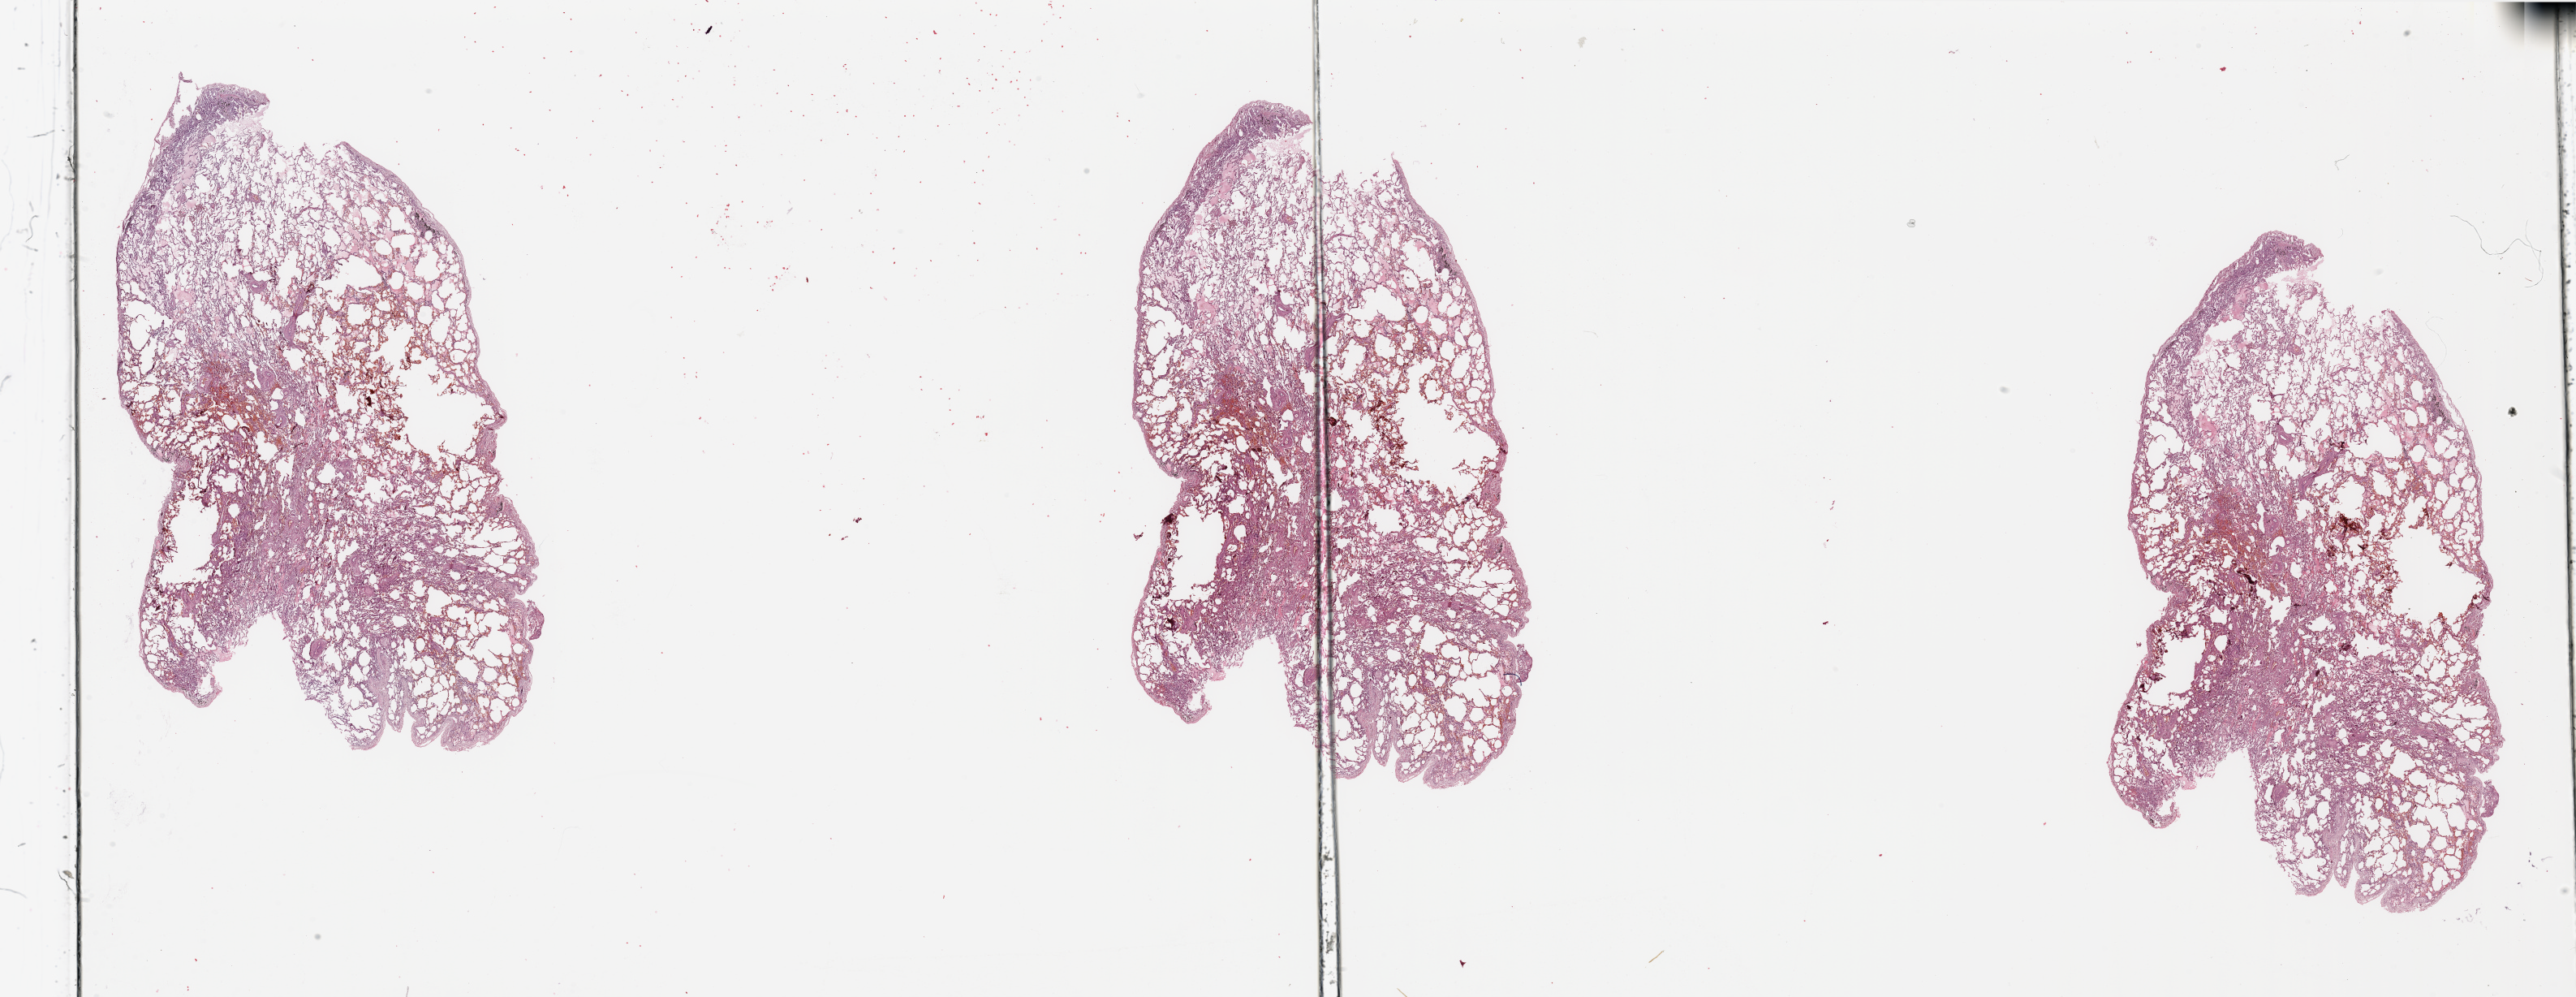
Whole-slide histology image, H&E-stained — shown as a low-resolution overview of the whole scanned area (about 50.2 x 19.4 mm, acquisition: 20x scan), normal (non-tumour) tissue sample, lung. 64-year-old male patient.
* this section: normal (non-tumour) tissue from the same patient
* patient diagnosis: Squamous cell carcinoma, NOS